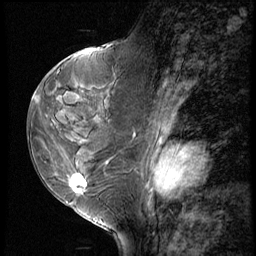
Breast MRI (dynamic contrast-enhanced), one sagittal slice. Slice 30 of 60 in the series (ordered by position). 3 images stored at this slice position (order not interpretable as contrast timing). 1.5 T. TE 4.2 ms, TR 8.9 ms. 2.5 mm slice thickness. 256 × 256 image matrix, field of view 200 × 200 mm. Patient: female, 50 years. Case-level facts recorded for this patient, not image findings: setting: breast cancer imaged before/during neoadjuvant chemotherapy; receptor status: HR-positive, HER2-negative.
Annotated regions visible in this slice (semi-automatically segmented with operator editing):
- analysis volume of interest (the breast-tissue region the enhancement analysis was run in; not a lesion): bounding box (x1, y1, x2, y2) in pixels: (38, 102, 118, 213)
- tumour enhancement mask (voxels above the 140 % enhancement threshold inside the analysis volume of interest): (70, 174, 88, 193)